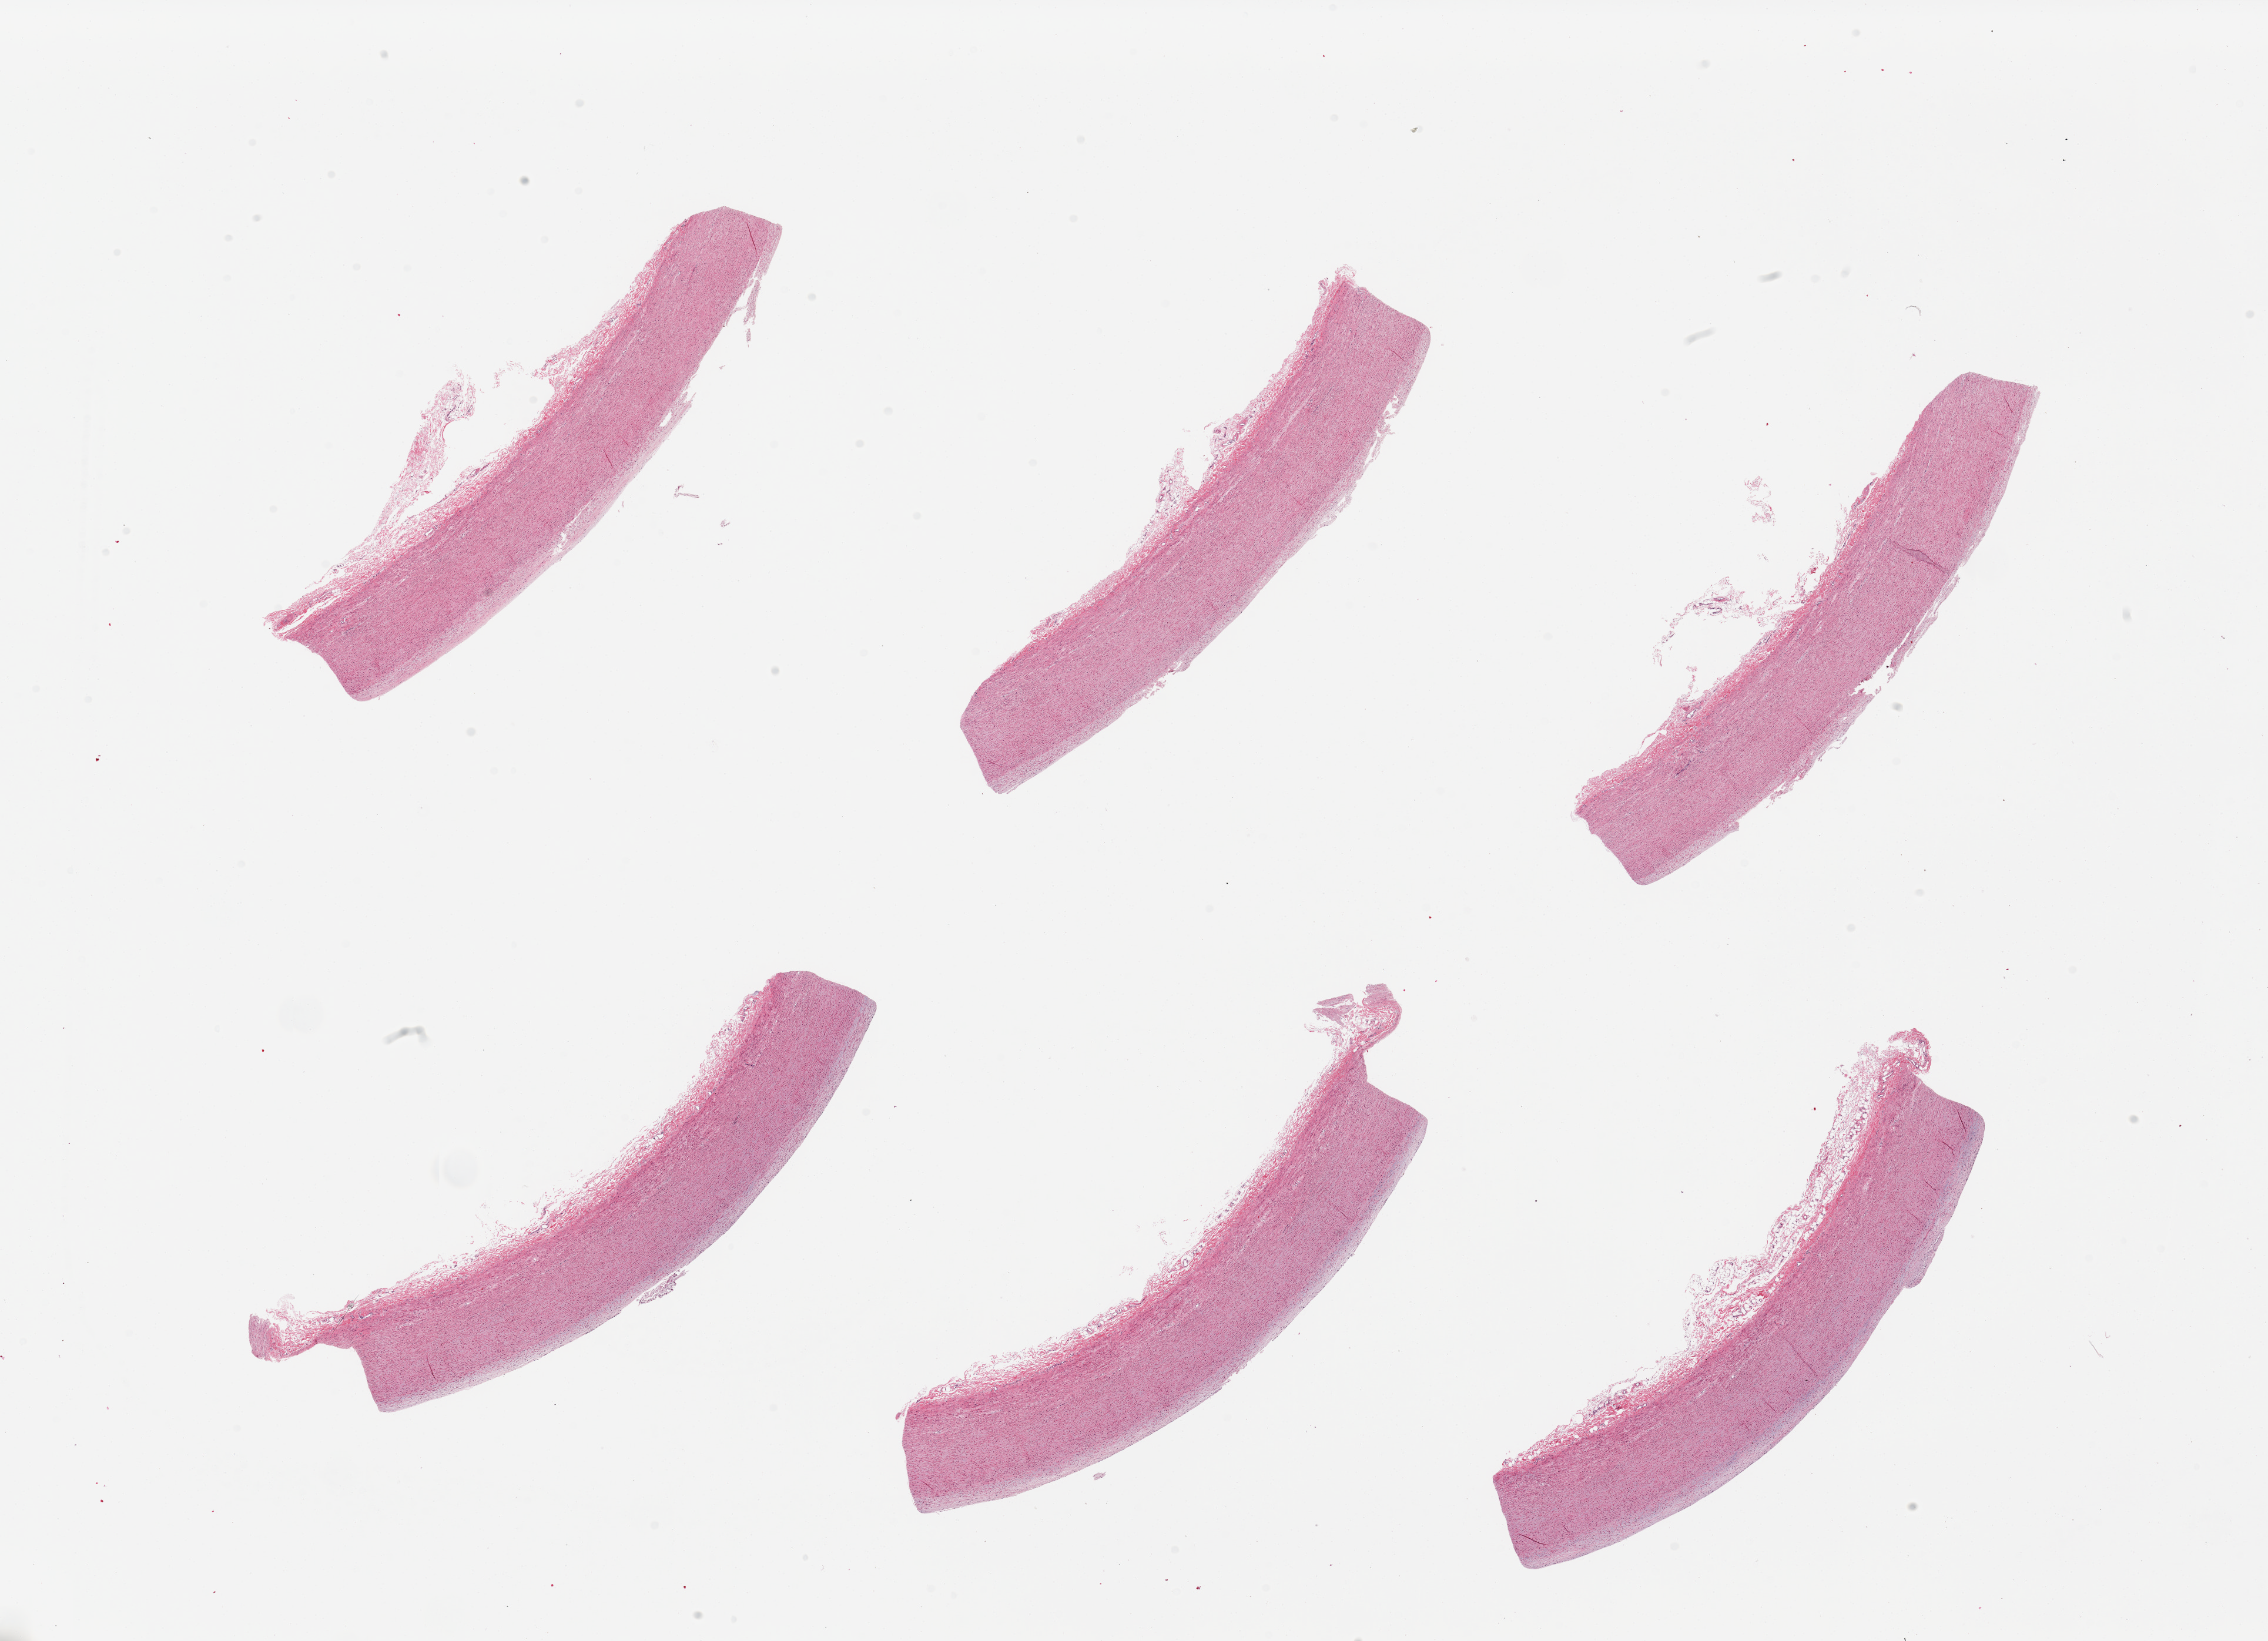
Digitized hematoxylin and eosin (H&E)-stained section, brightfield — a low-resolution overview of the entire scanned area, about 30.5 x 22.1 mm, PAXgene-fixed paraffin-embedded (PFPE) section, section of aorta (target tissue), tissue donor sample. Donor sex: female.
- pathologist's review note for this sample: 6 pieces, ~0.5mm adherent serosal on most sections